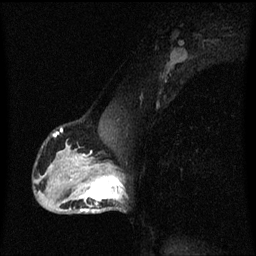
Breast MRI (dynamic contrast-enhanced), one sagittal slice; position 37 of 60 along the scan axis; dynamic contrast-enhanced series, image 2 of 3 at this slice position (ordered by acquisition); 1.5 T; TE 4.2 ms, TR 8.4 ms; 2 mm slice thickness; 256 × 256 image matrix, field of view 200 × 200 mm. Patient: female, 40 years.
Annotated regions visible in this slice (semi-automatically segmented with operator editing):
- analysis volume of interest (the breast-tissue region the enhancement analysis was run in; not a lesion): bounding box (x1, y1, x2, y2) in pixels: (76, 172, 125, 213)
- tumour enhancement mask (voxels above the 70 % enhancement threshold inside the analysis volume of interest): (76, 172, 125, 213)